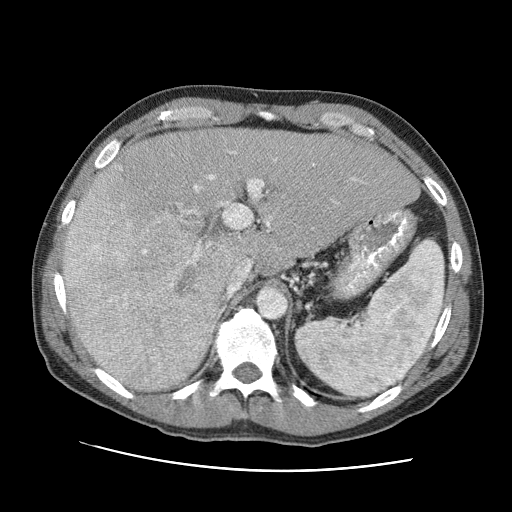
Contrast-enhanced abdominal CT (liver protocol), one axial slice; position 62 of 95 along the scan axis; reconstruction kernel STANDARD; one of 2 acquisitions stored at this slice position; soft-tissue window (W 400 / L 40 HU); 2.5 mm slice thickness; 512 × 512 image matrix, field of view 360 × 360 mm. From the clinical record (not read from this slice): diagnosis: hepatocellular carcinoma (patient treated with transarterial chemoembolisation; whether this scan precedes or follows treatment is not stated here); TNM stage (as recorded): Stage-IVA; Child-Pugh class: A; tumour differentiation: moderately differentiated; tumour nodularity: multinodular.
Structures marked on this image (semi-automatic segmentation, software-assisted and operator-edited):
- liver parenchyma outside the tumour (the mass and vessels are separate outlines, so this box may not span the whole liver): bounding box (x1, y1, x2, y2) in pixels: (62, 128, 420, 390)
- mass: (66, 143, 228, 388)
- liver vessels: (65, 151, 357, 289)